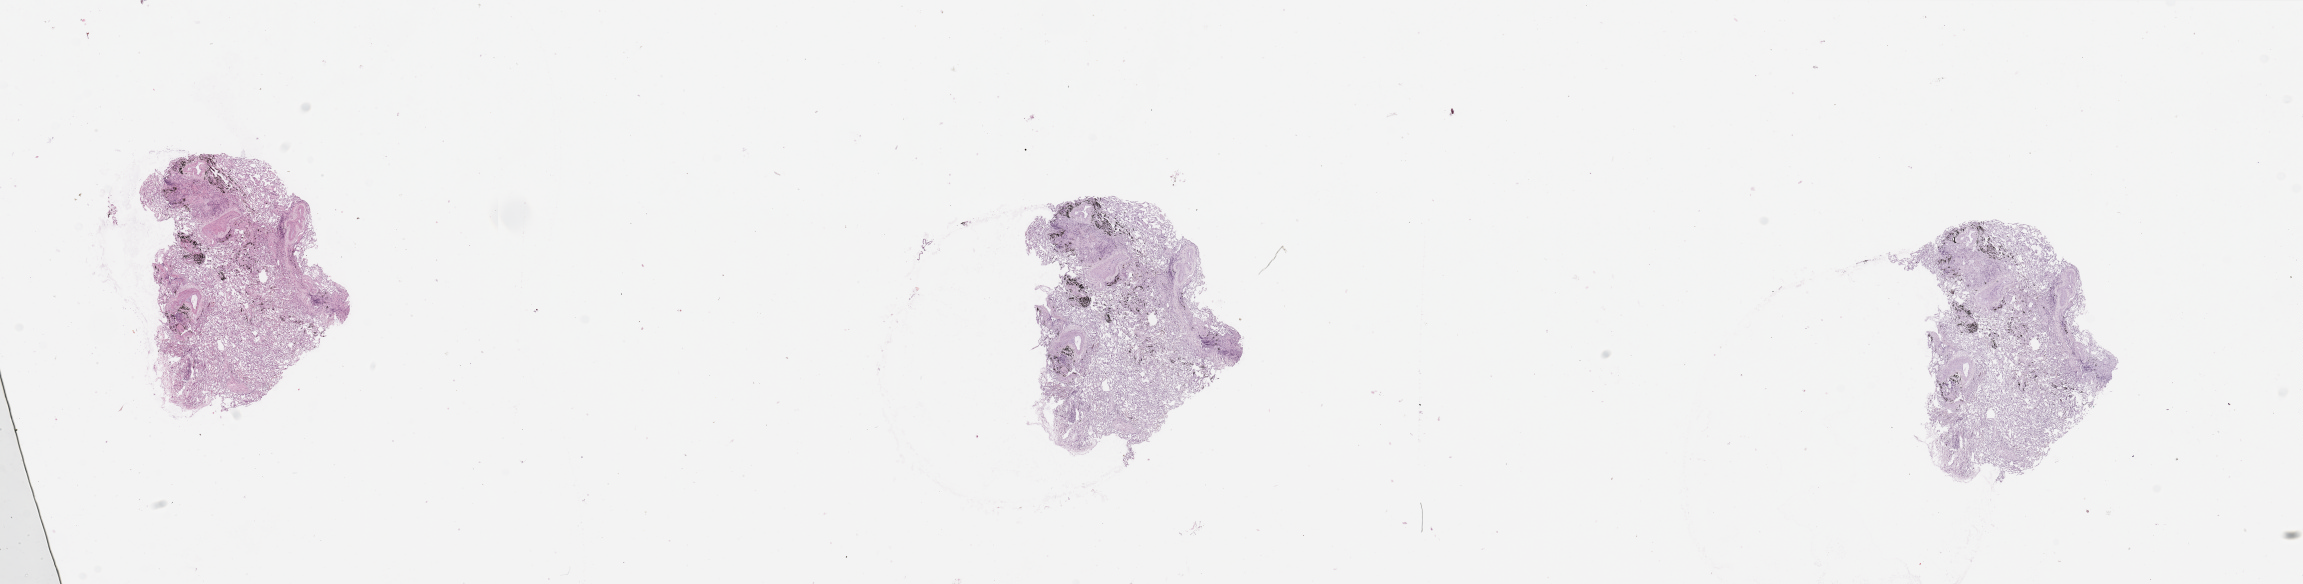
H&E whole-slide image, shown as a low-resolution overview of the whole scanned area (about 36.4 x 9.2 mm); normal (non-tumour) tissue sample, sampled site: lung. Patient: male, age 76 years.
• this section: normal (non-tumour) tissue from the same patient
• patient diagnosis: Adenocarcinoma, NOS